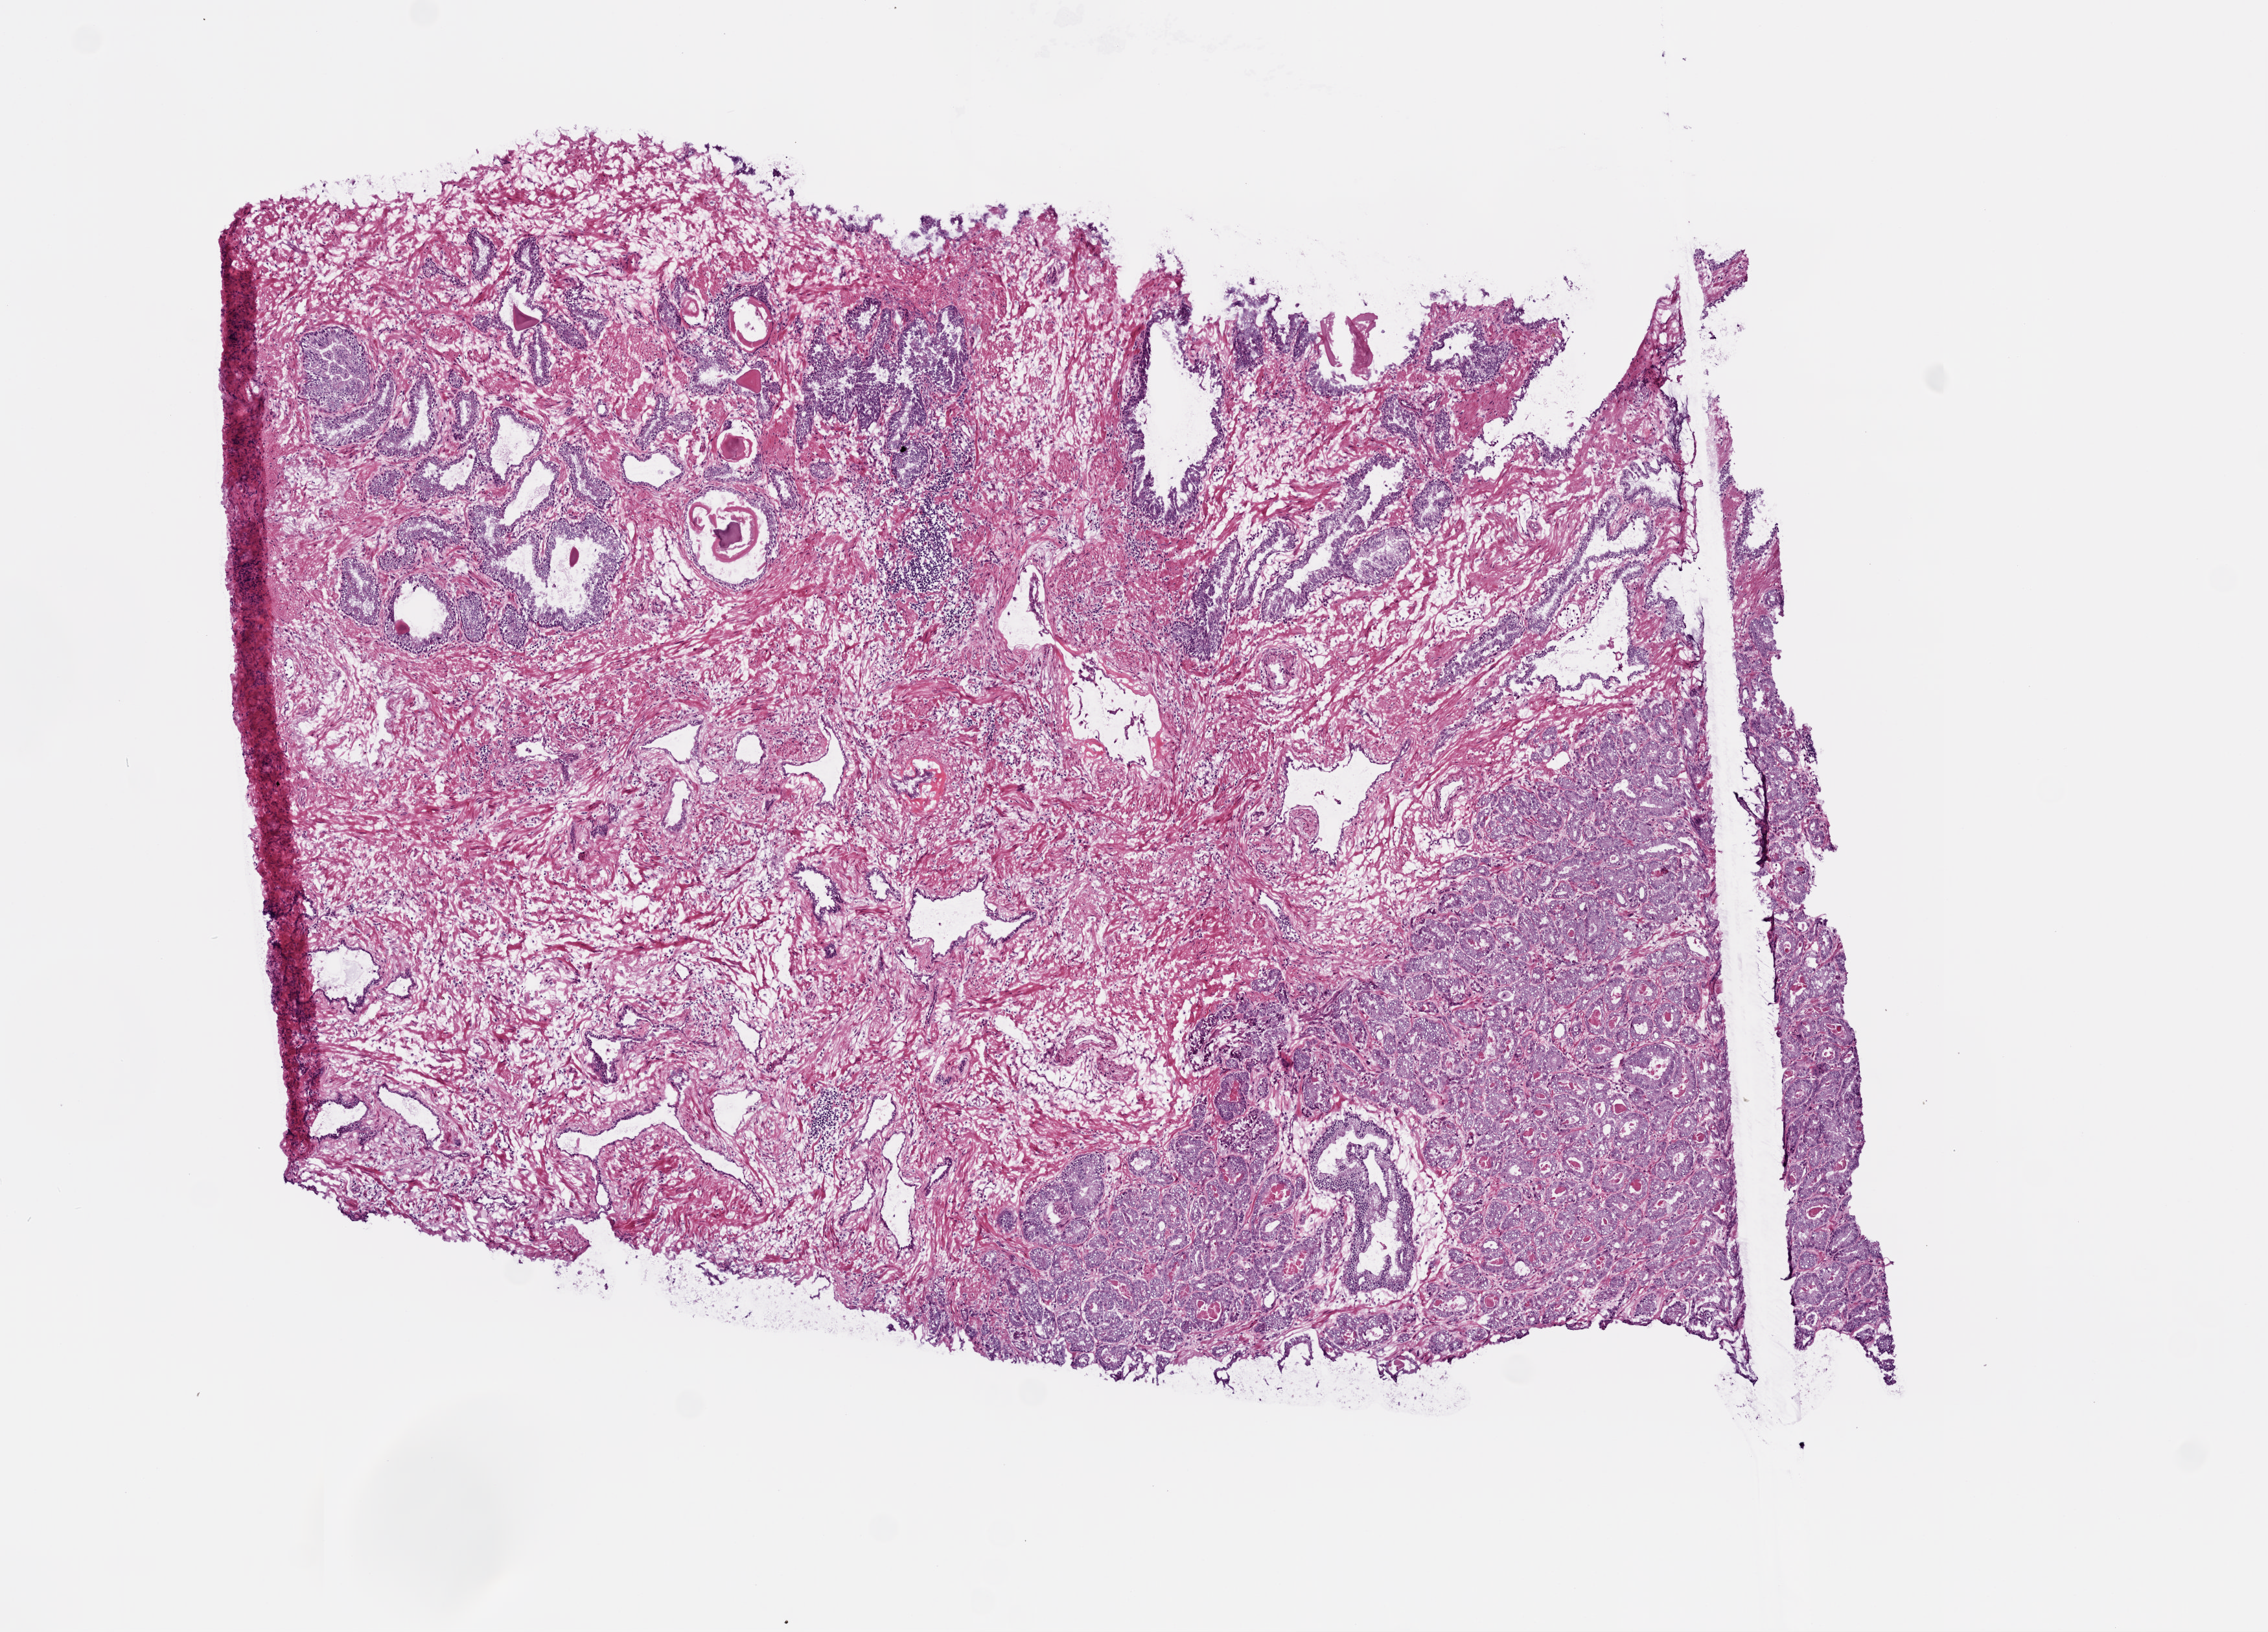
Hematoxylin and eosin (H&E) stained whole-slide image — a low-resolution overview of the entire scanned area, about 7.0 x 5.1 mm (acquisition: 20x scan), frozen section, sample: primary tumour, prostate. Male patient; age at initial diagnosis 66 years. Gleason score: 7 (4+3). Slide review estimates, as recorded: tumour cells 25%, tumour nuclei 40%, normal cells 20%, stromal cells 55%, necrosis 0%. Infiltration values recorded for this section: lymphocyte infiltration 2%, monocyte infiltration 0%, neutrophil infiltration 0%.
- lymph nodes positive (case pathology): 0 of 19 examined
- diagnosis: Acinar cell carcinoma
- laterality: bilateral